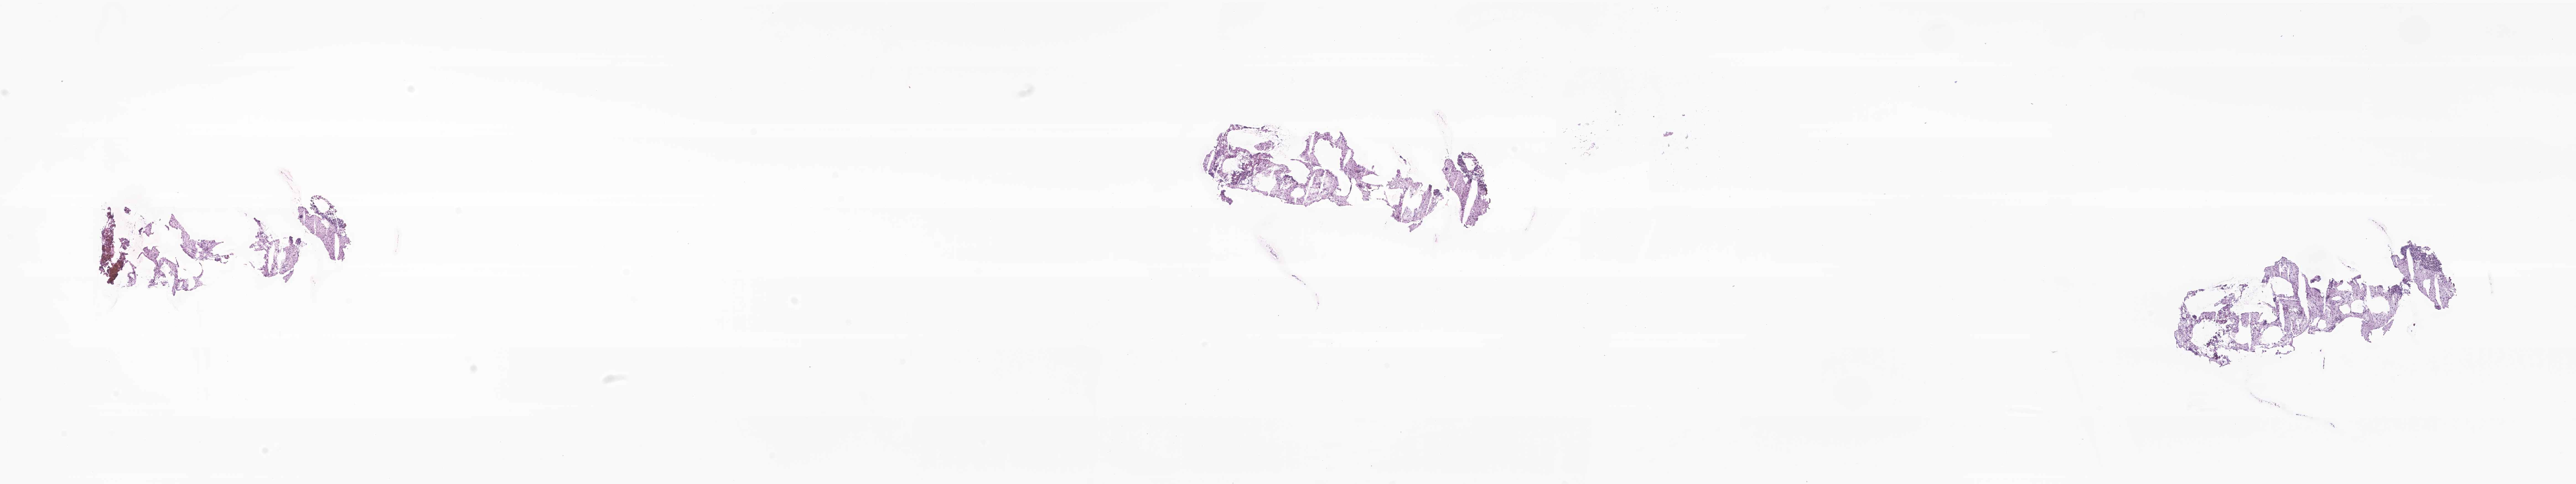
Digitized hematoxylin and eosin (H&E)-stained section of tumor tissue from the brain, a low-resolution overview of the entire scanned area, about 39.2 x 7.4 mm. Frozen section. Female patient, age 85 months.
Diagnosis: Medulloblastoma, NOS.